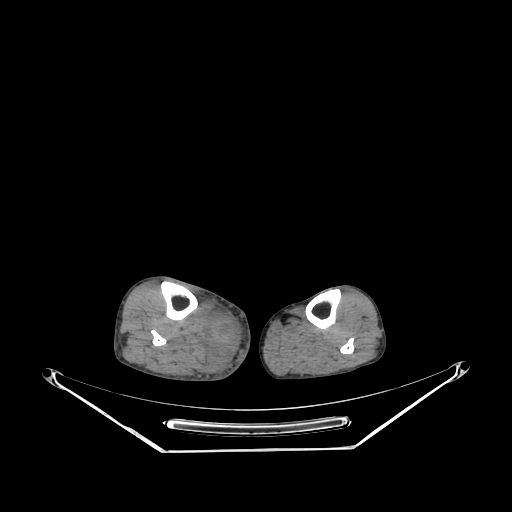
CT of an extremity soft-tissue mass (from a PET/CT study), one axial slice. Slice 127 of 267 in the series (ordered by position). Reconstruction kernel SOFT. 140 kVp. Soft-tissue window (W 400 / L 40 HU). 3.75 mm slice thickness. 512 × 512 image matrix. Male patient. Case-level facts recorded for this patient, not image findings: histological type: pleiomorphic liposarcoma; grade: high; site of the primary tumour: right calf.
Structures marked on this image (expert contour drawn on MRI and transferred to this co-registered scan by the dataset authors):
- gross tumour volume including surrounding oedema: bounding box <205,307,241,373> (left, top, right, bottom; pixels)
- gross tumour volume (mass): <208,317,234,344>